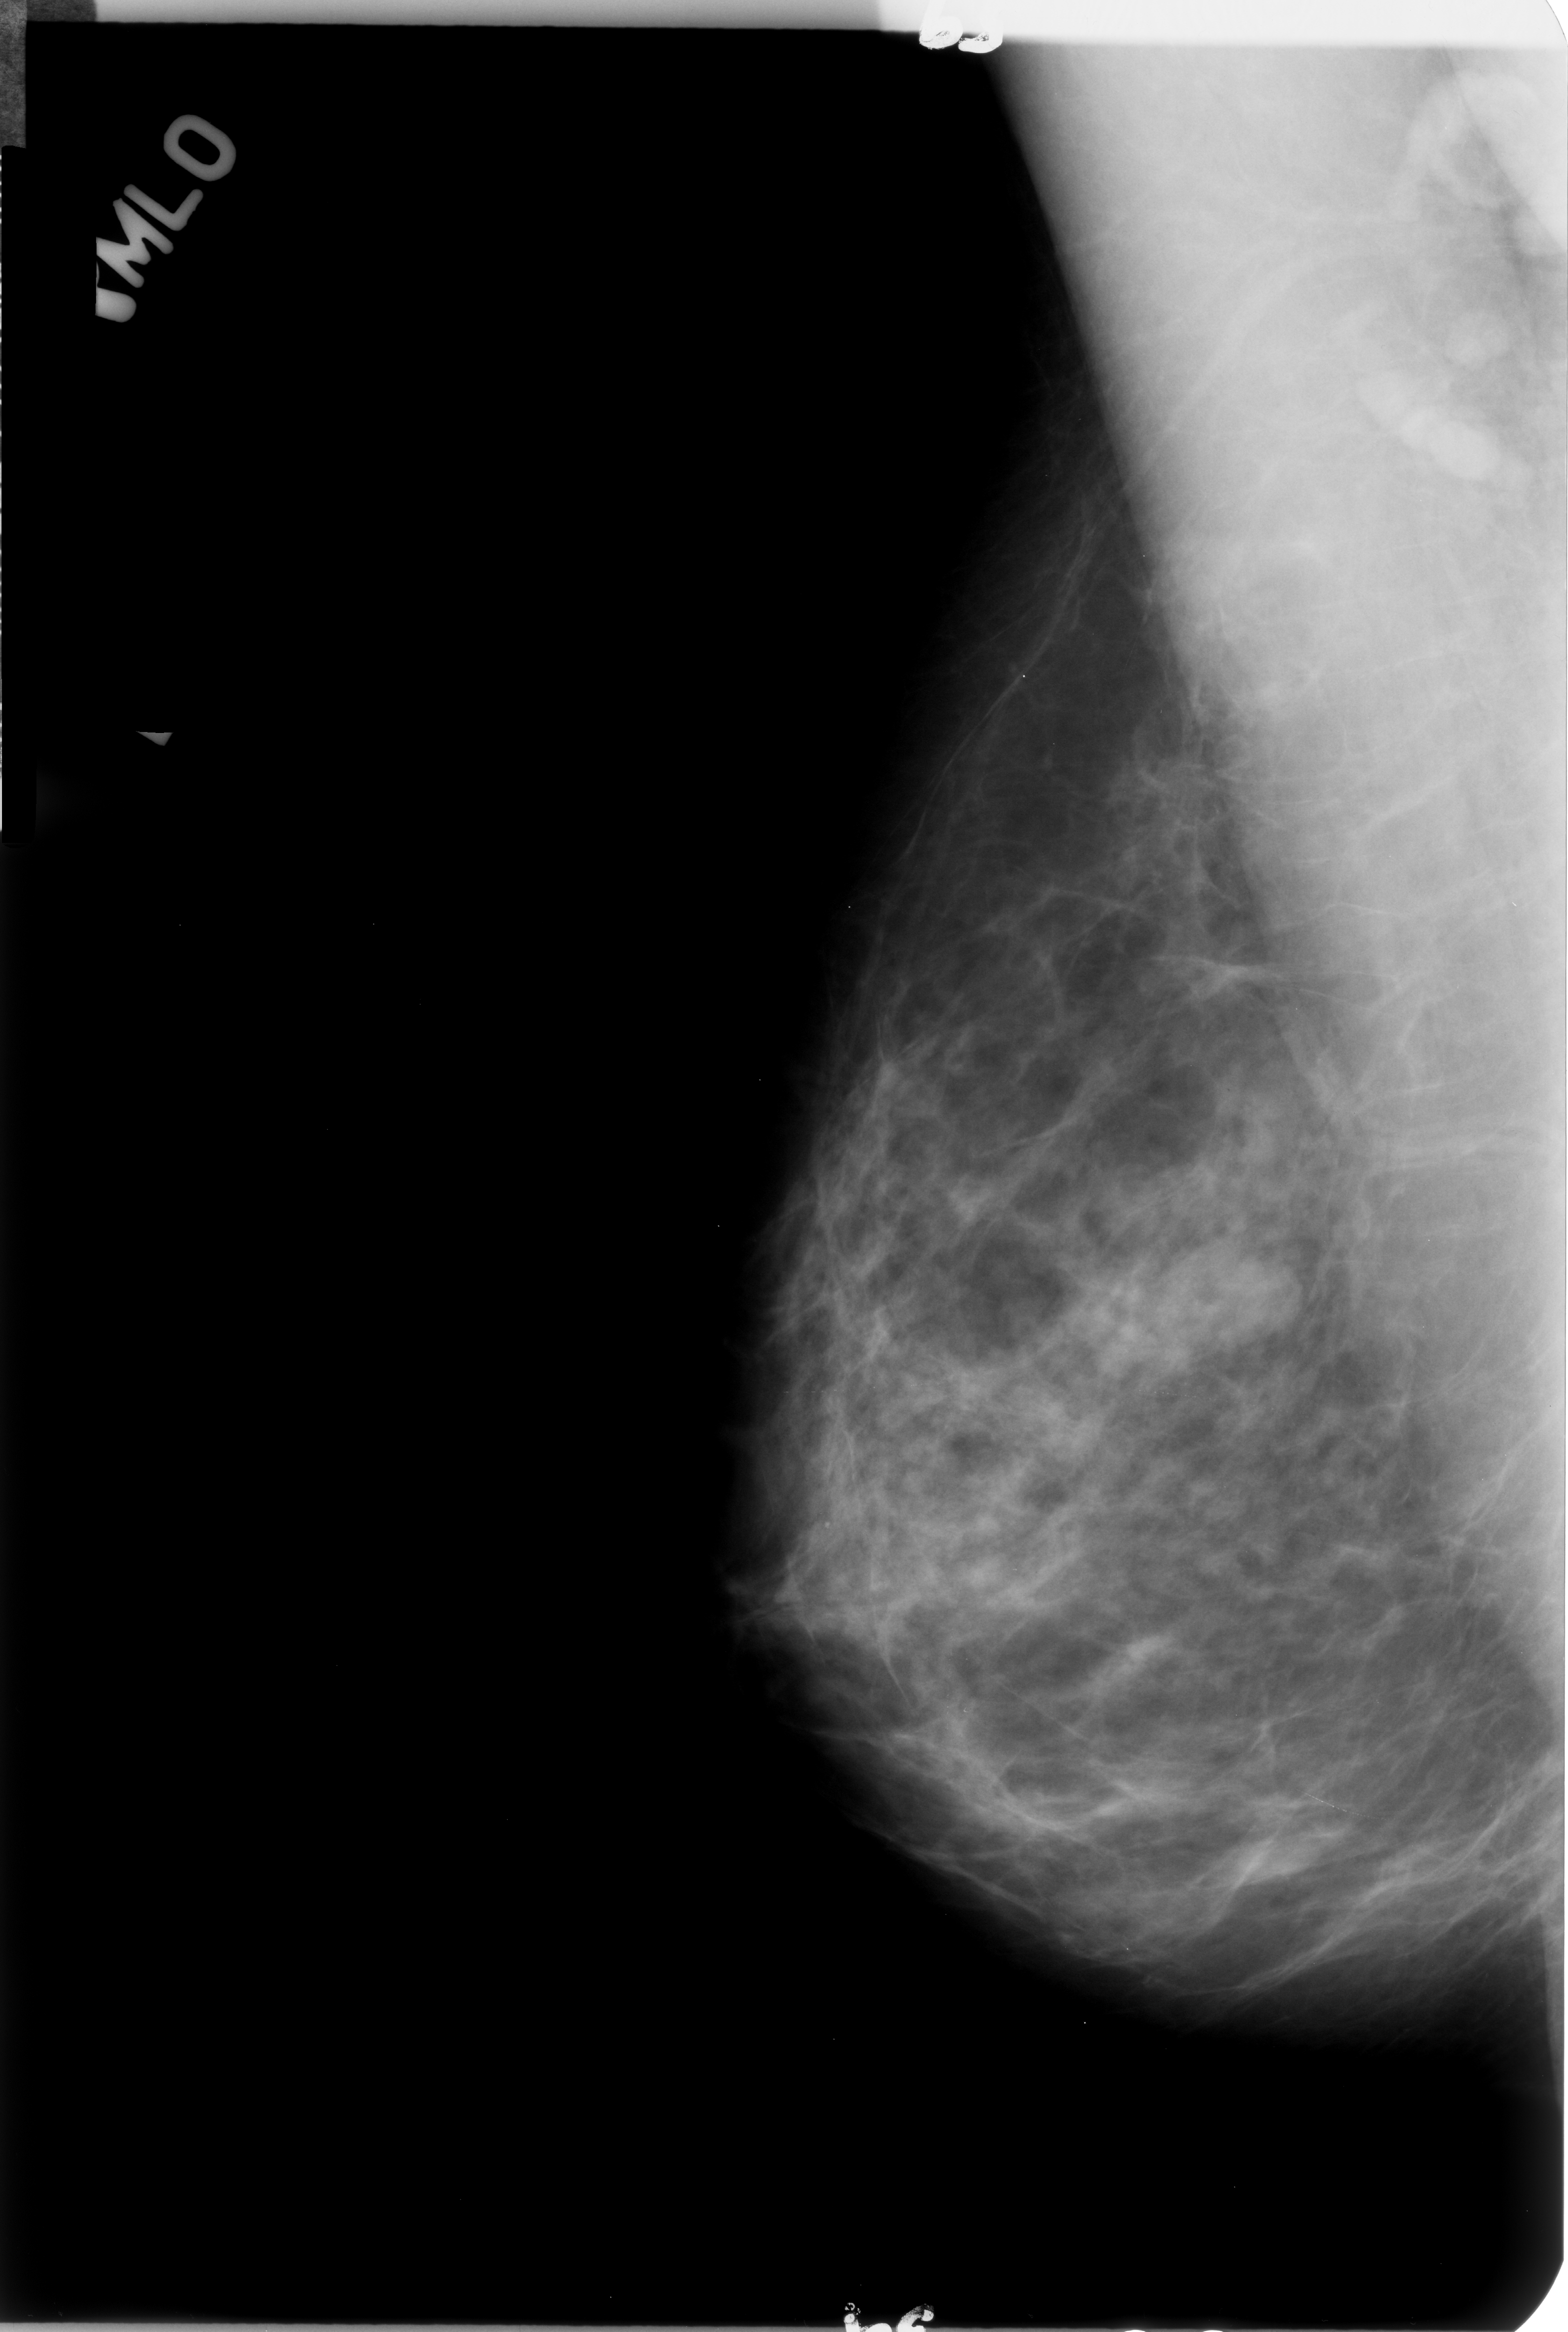
Mammogram (digitized film); right breast; MLO view; breast composition: heterogeneously dense (BI-RADS density category 3 of 4); 1568 × 2332 image matrix.
Expert-marked regions of interest on this film, with their recorded descriptors:
- mass, shape oval, margins circumscribed; BI-RADS assessment category 3; subtlety rating 3 on a 1 (subtle) to 5 (obvious) scale; pathology (as recorded): benign: box from (x=1156, y=1211) to (x=1307, y=1361) px